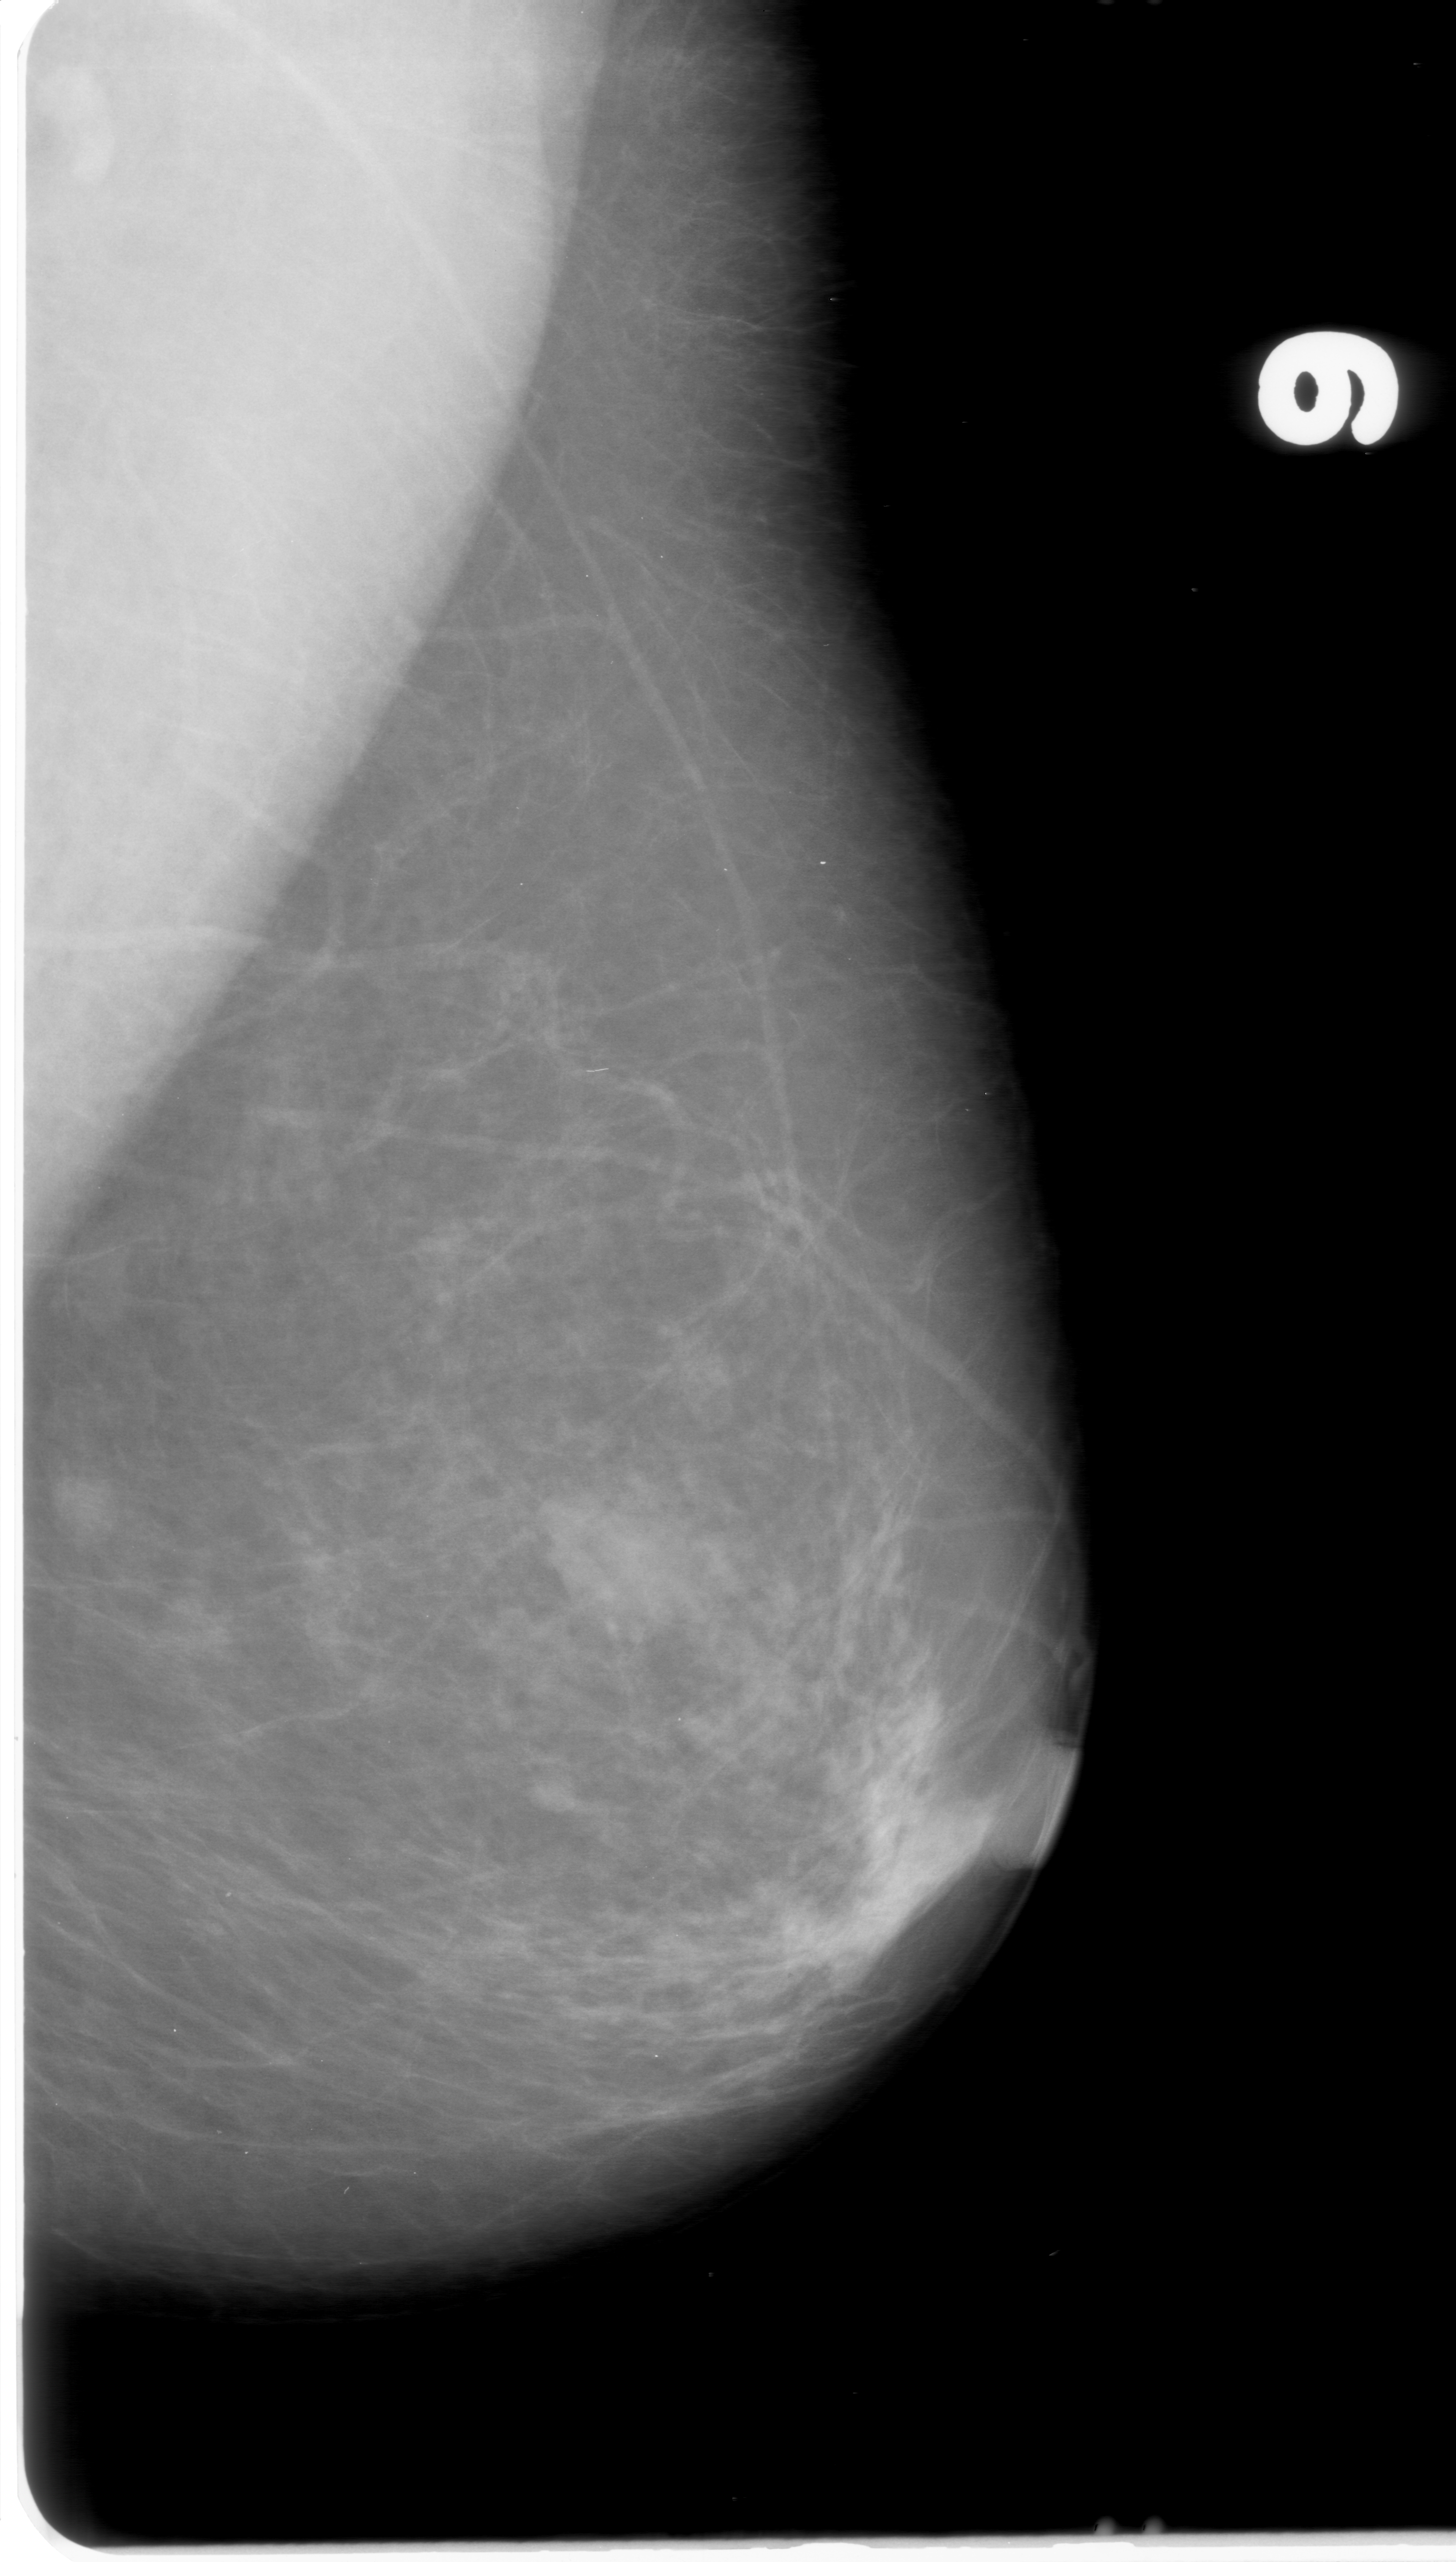
Digitized screen-film mammogram, left breast, mediolateral oblique (MLO) view, breast composition: almost entirely fatty (BI-RADS density category 1 of 4).
- Abnormality record for this image: mass, shape oval, margins obscured; BI-RADS assessment category 0 (incomplete: needs additional imaging); subtlety rating 5 on a 1 (subtle) to 5 (obvious) scale; pathology (as recorded): benign.